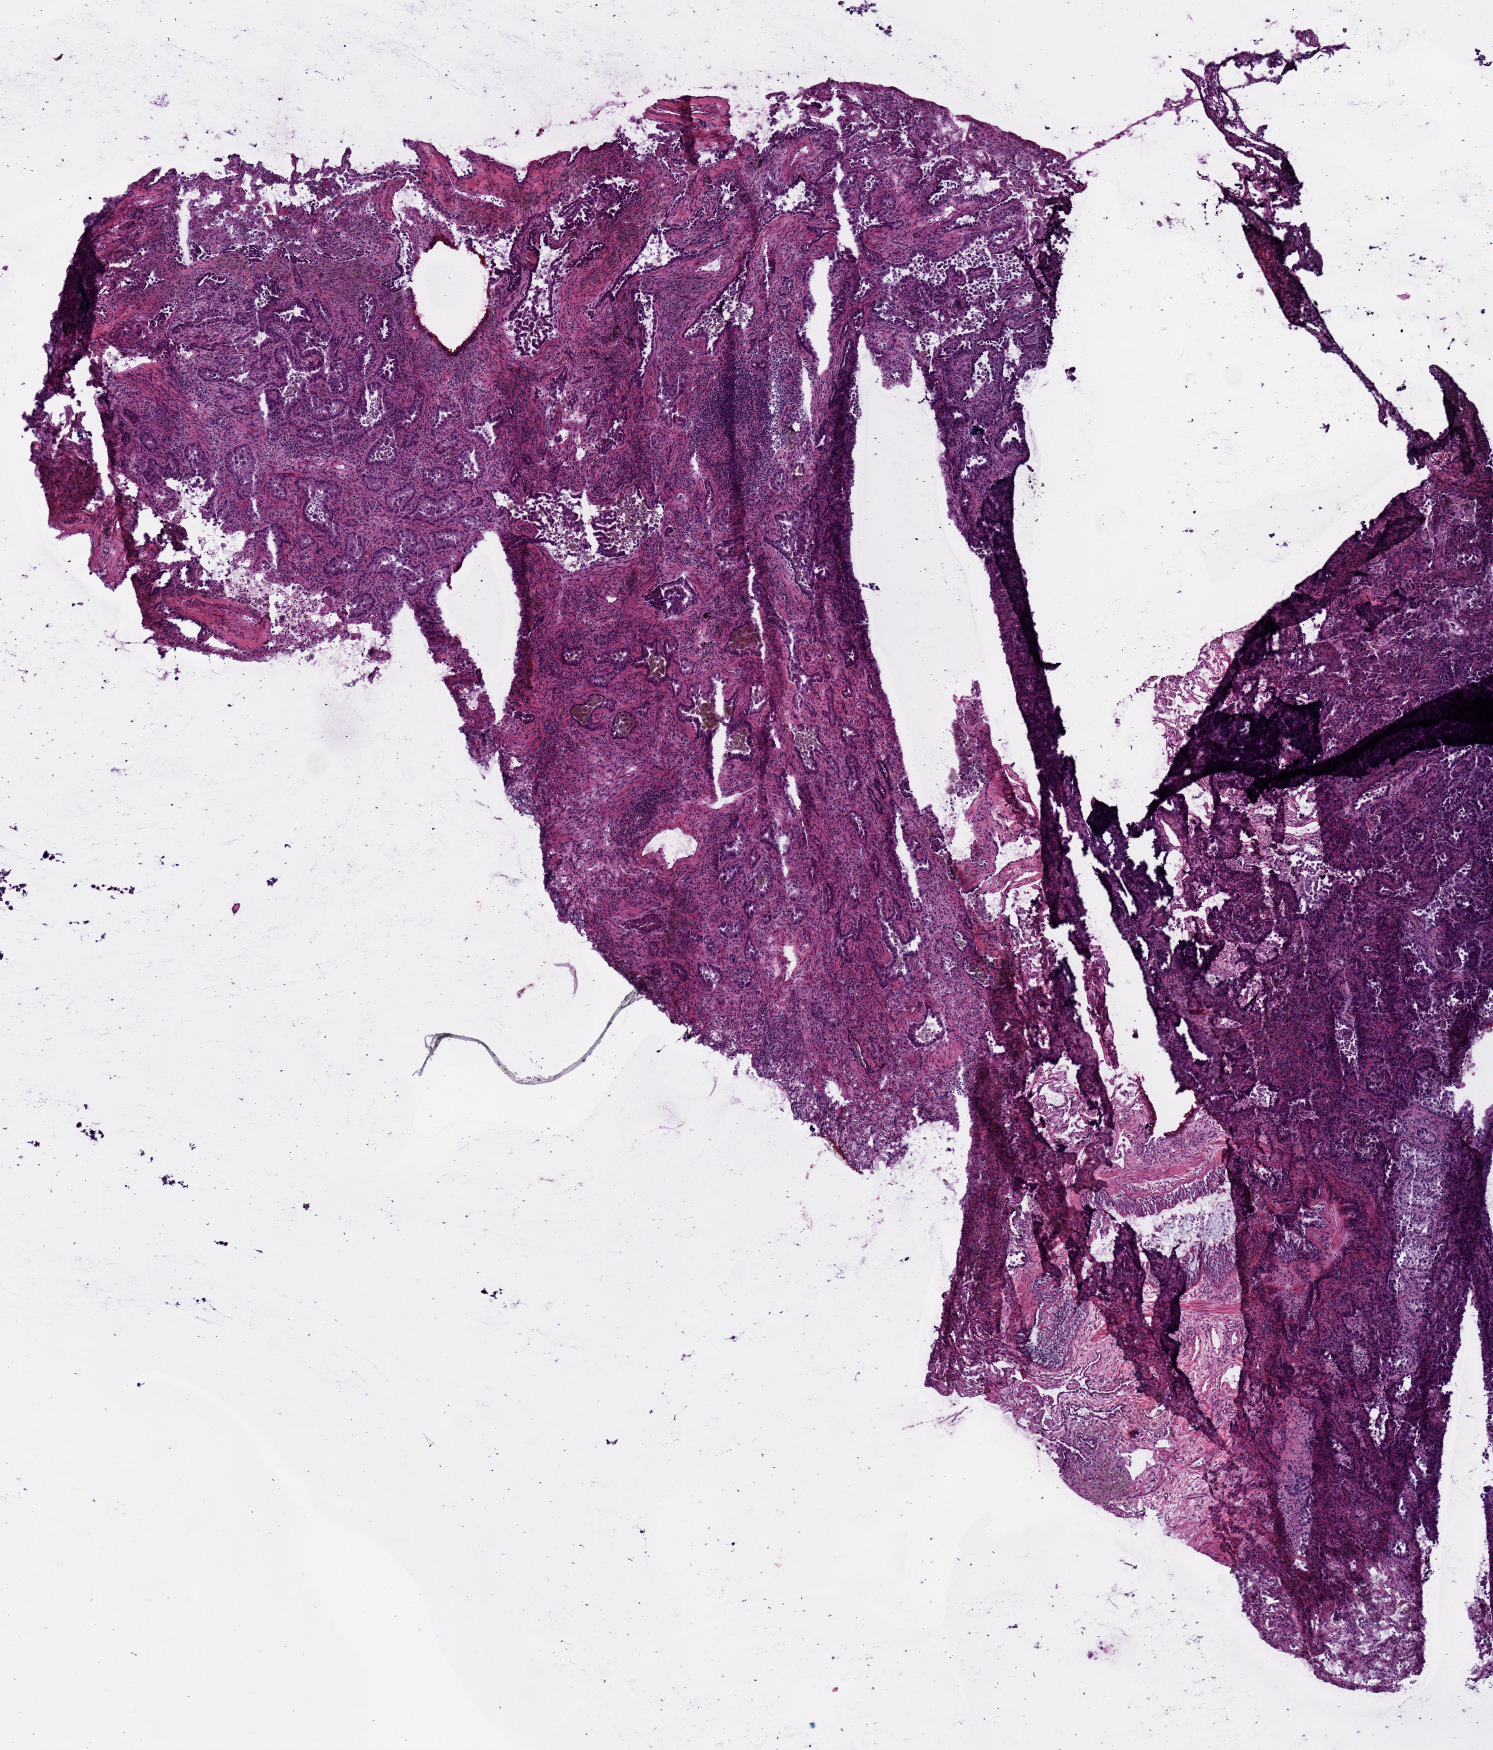
Digitized H&E tissue section (whole slide) — shown as a low-resolution overview of the whole scanned area (about 5.9 x 6.9 mm, acquisition: 20x scan). Frozen section from the top of the tissue portion. Lung, primary tumour sample. Patient: male, age at initial diagnosis 58 years. Composition of this section per pathologist review: tumour cells 75%, tumour nuclei 60%, normal cells 0%, stromal cells 25%, necrosis 0%.
AJCC pathologic stage: IB. Pathologic diagnosis: Adenocarcinoma, NOS.